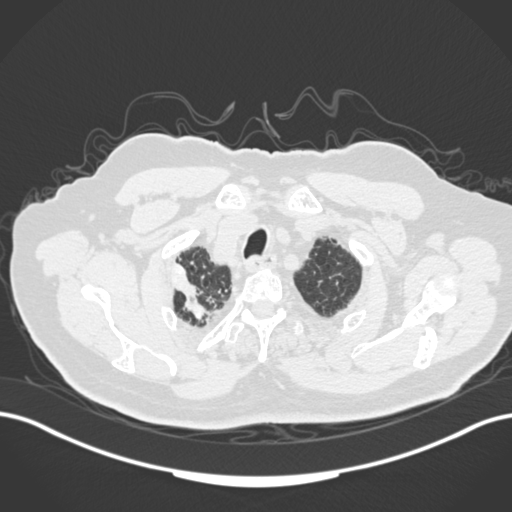
Chest CT, one axial slice; slice 154 of 205 in the series (ordered by position); 120 kVp; lung window (W 1500 / L -600 HU); 1 mm slice thickness; 512 × 512 image matrix, field of view 400 × 400 mm. Male patient, age 72 years. From the clinical record (not read from this slice): clinical TNM (as recorded): T1a N0 M0.
Annotated regions visible in this slice (bounding box drawn by a radiologist):
- lung tumour (recorded histology: squamous cell carcinoma): box from (x=170, y=261) to (x=208, y=325) px